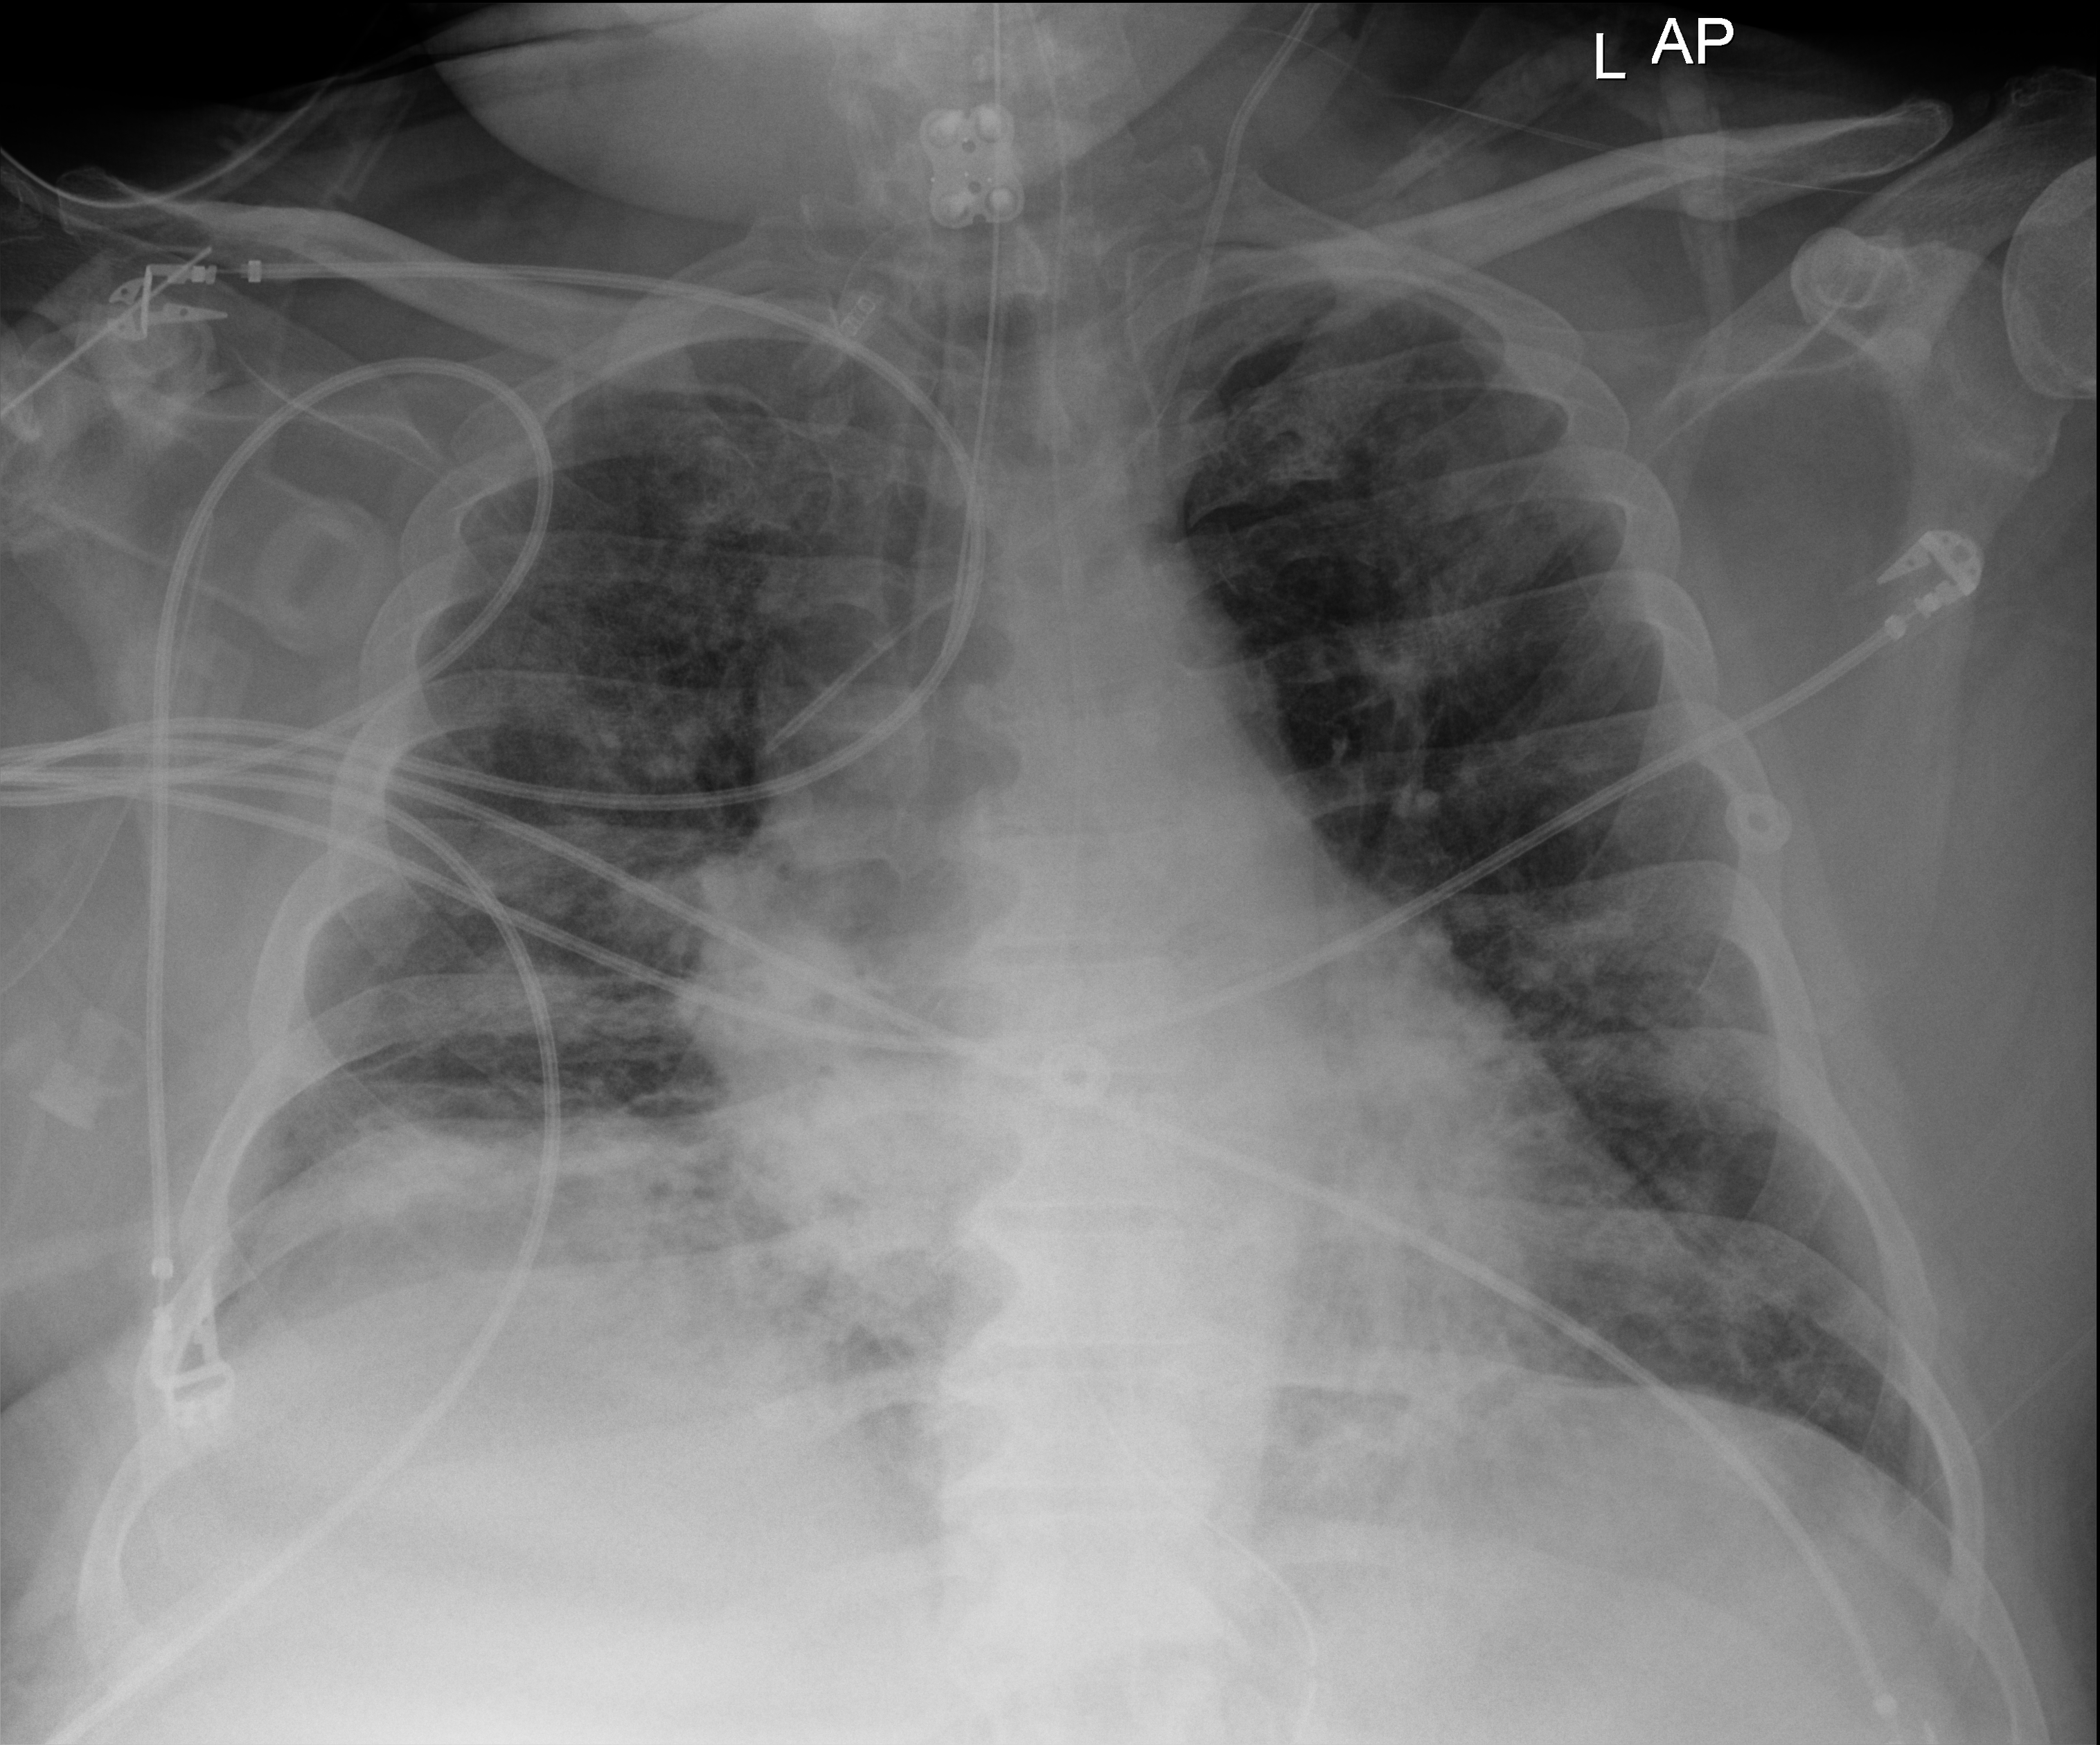
Bedside chest radiograph (digital radiography); anteroposterior (AP) projection. Patient hospitalised with COVID-19; male, aged 18–59 years.
Hospital-stay facts (about this admission, not read from this image; timing relative to this image not recorded): hypertension (admission record): yes.